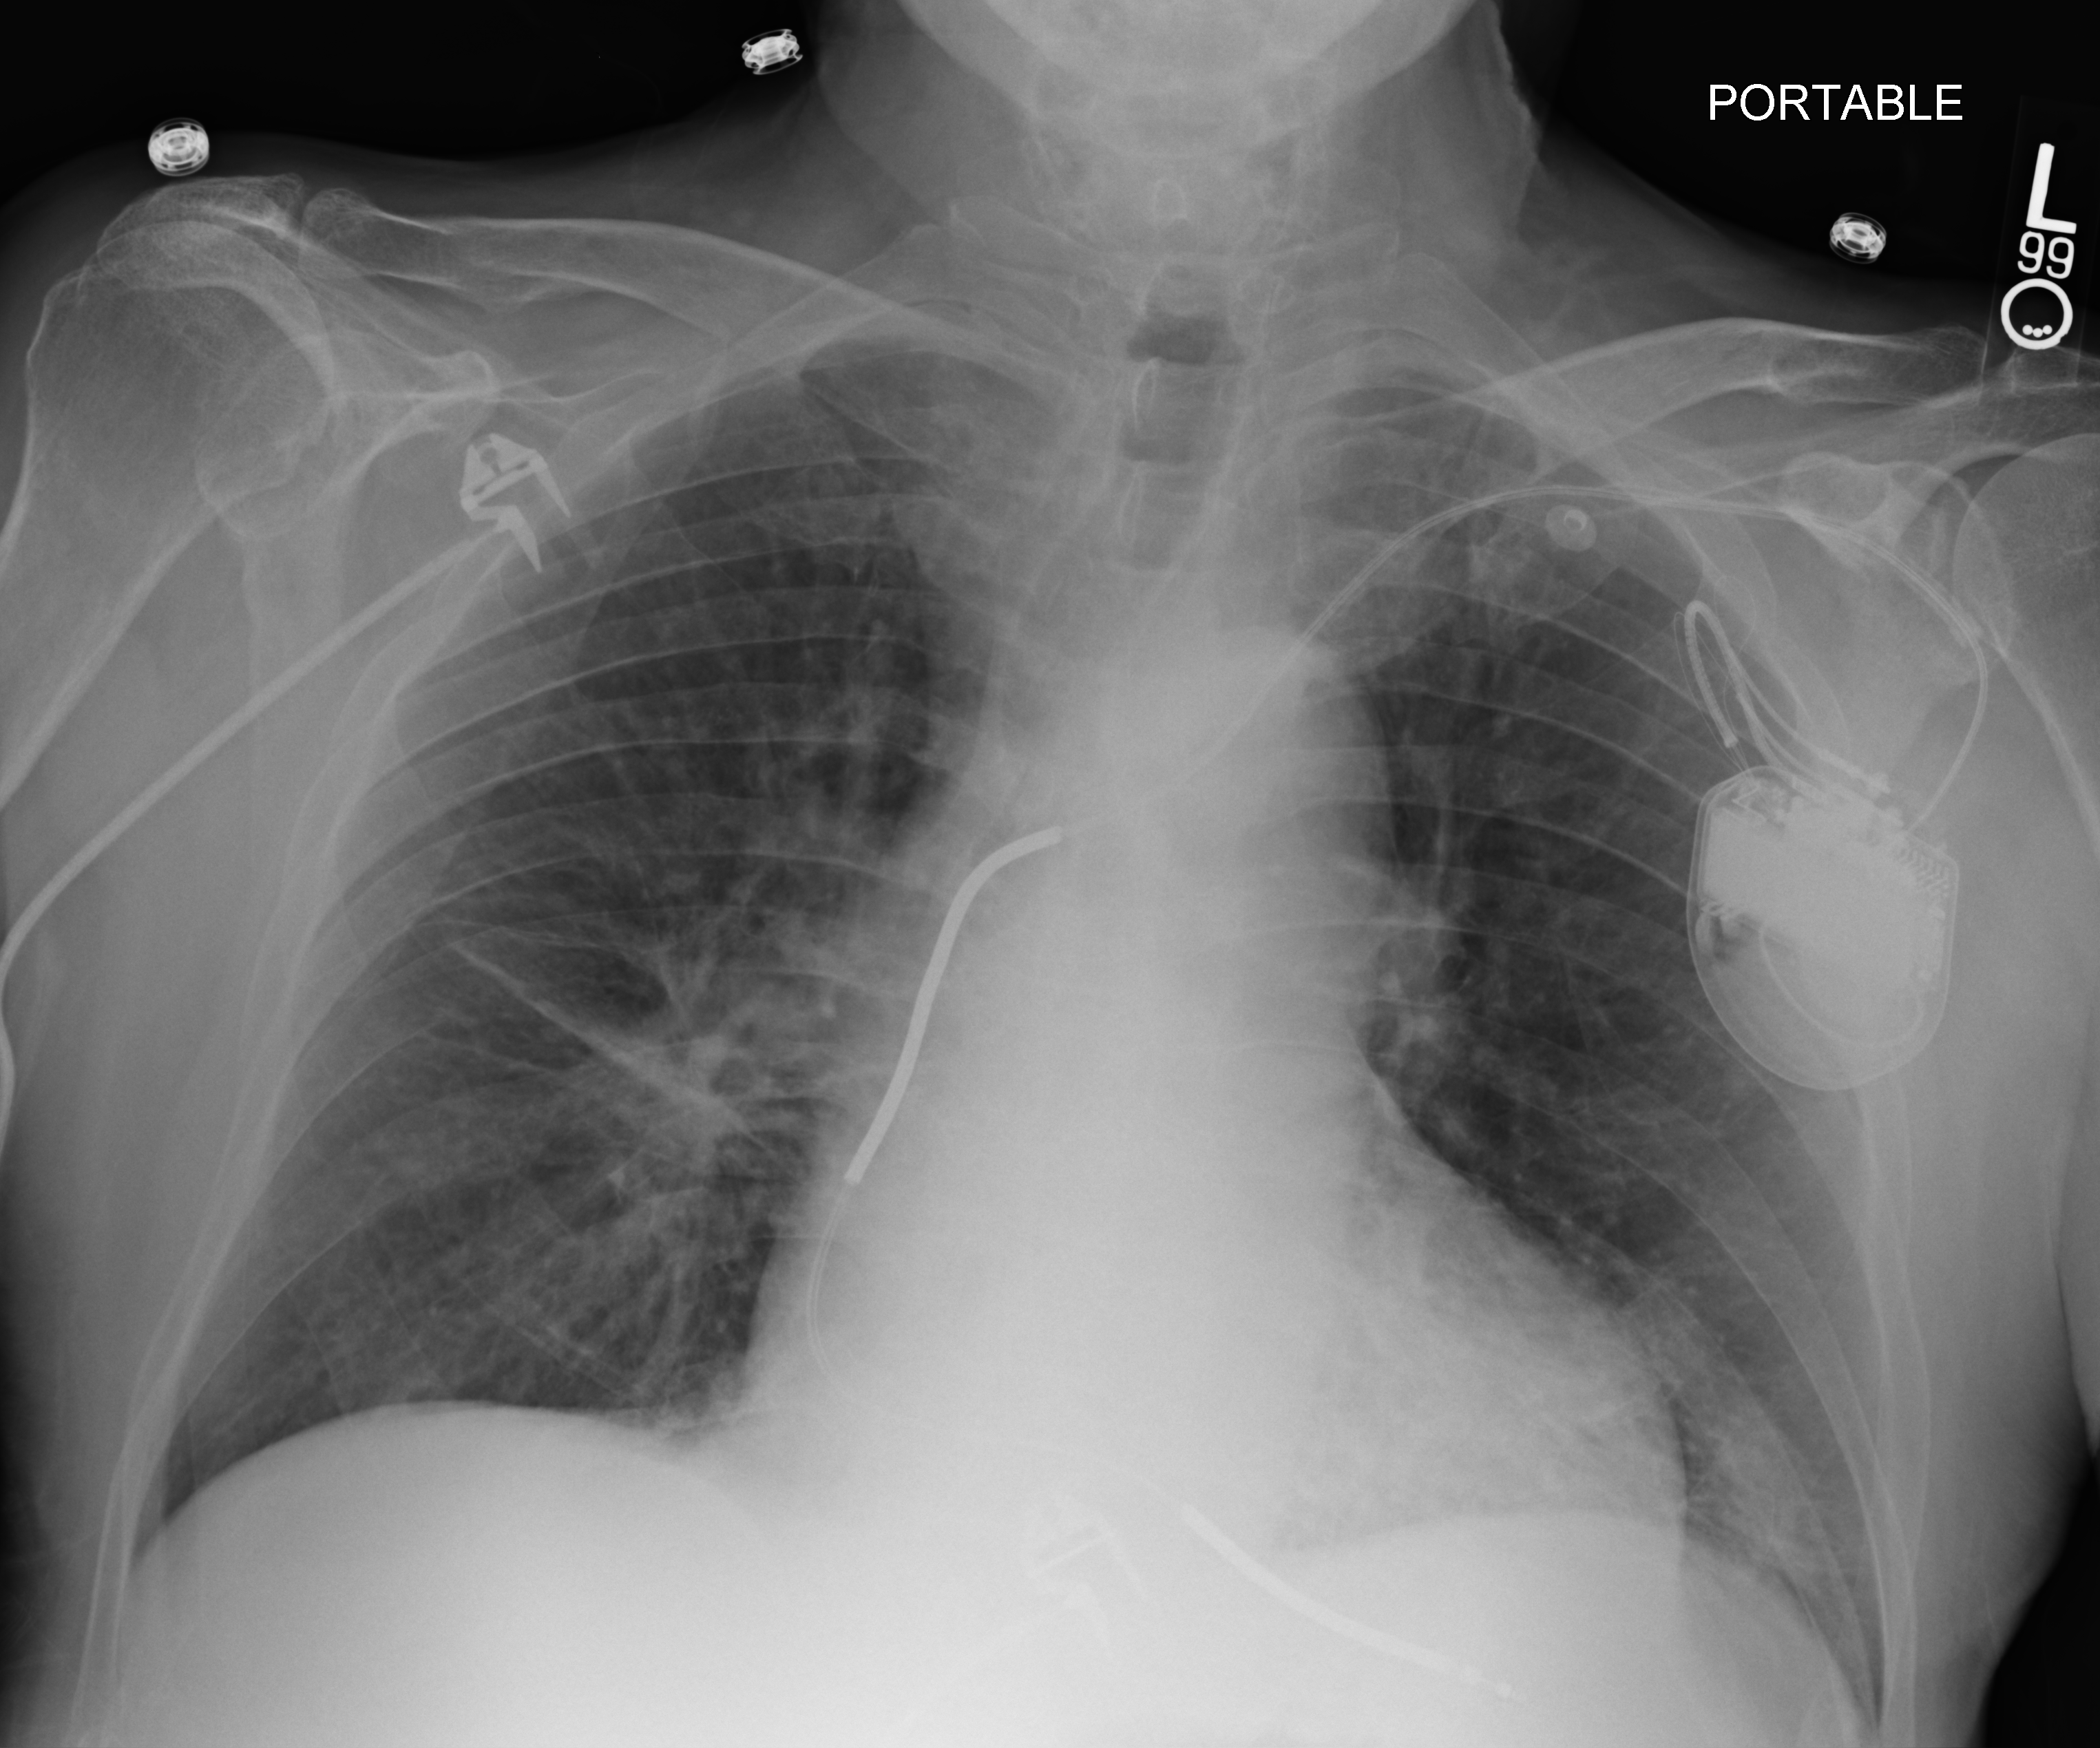
Portable chest radiograph, anteroposterior (AP) projection. Patient hospitalised with COVID-19; male, aged 75–90 years.
Admission-level facts for this patient (not findings on this image; timing relative to this image not recorded):
- admitted to intensive care during this hospital stay: no